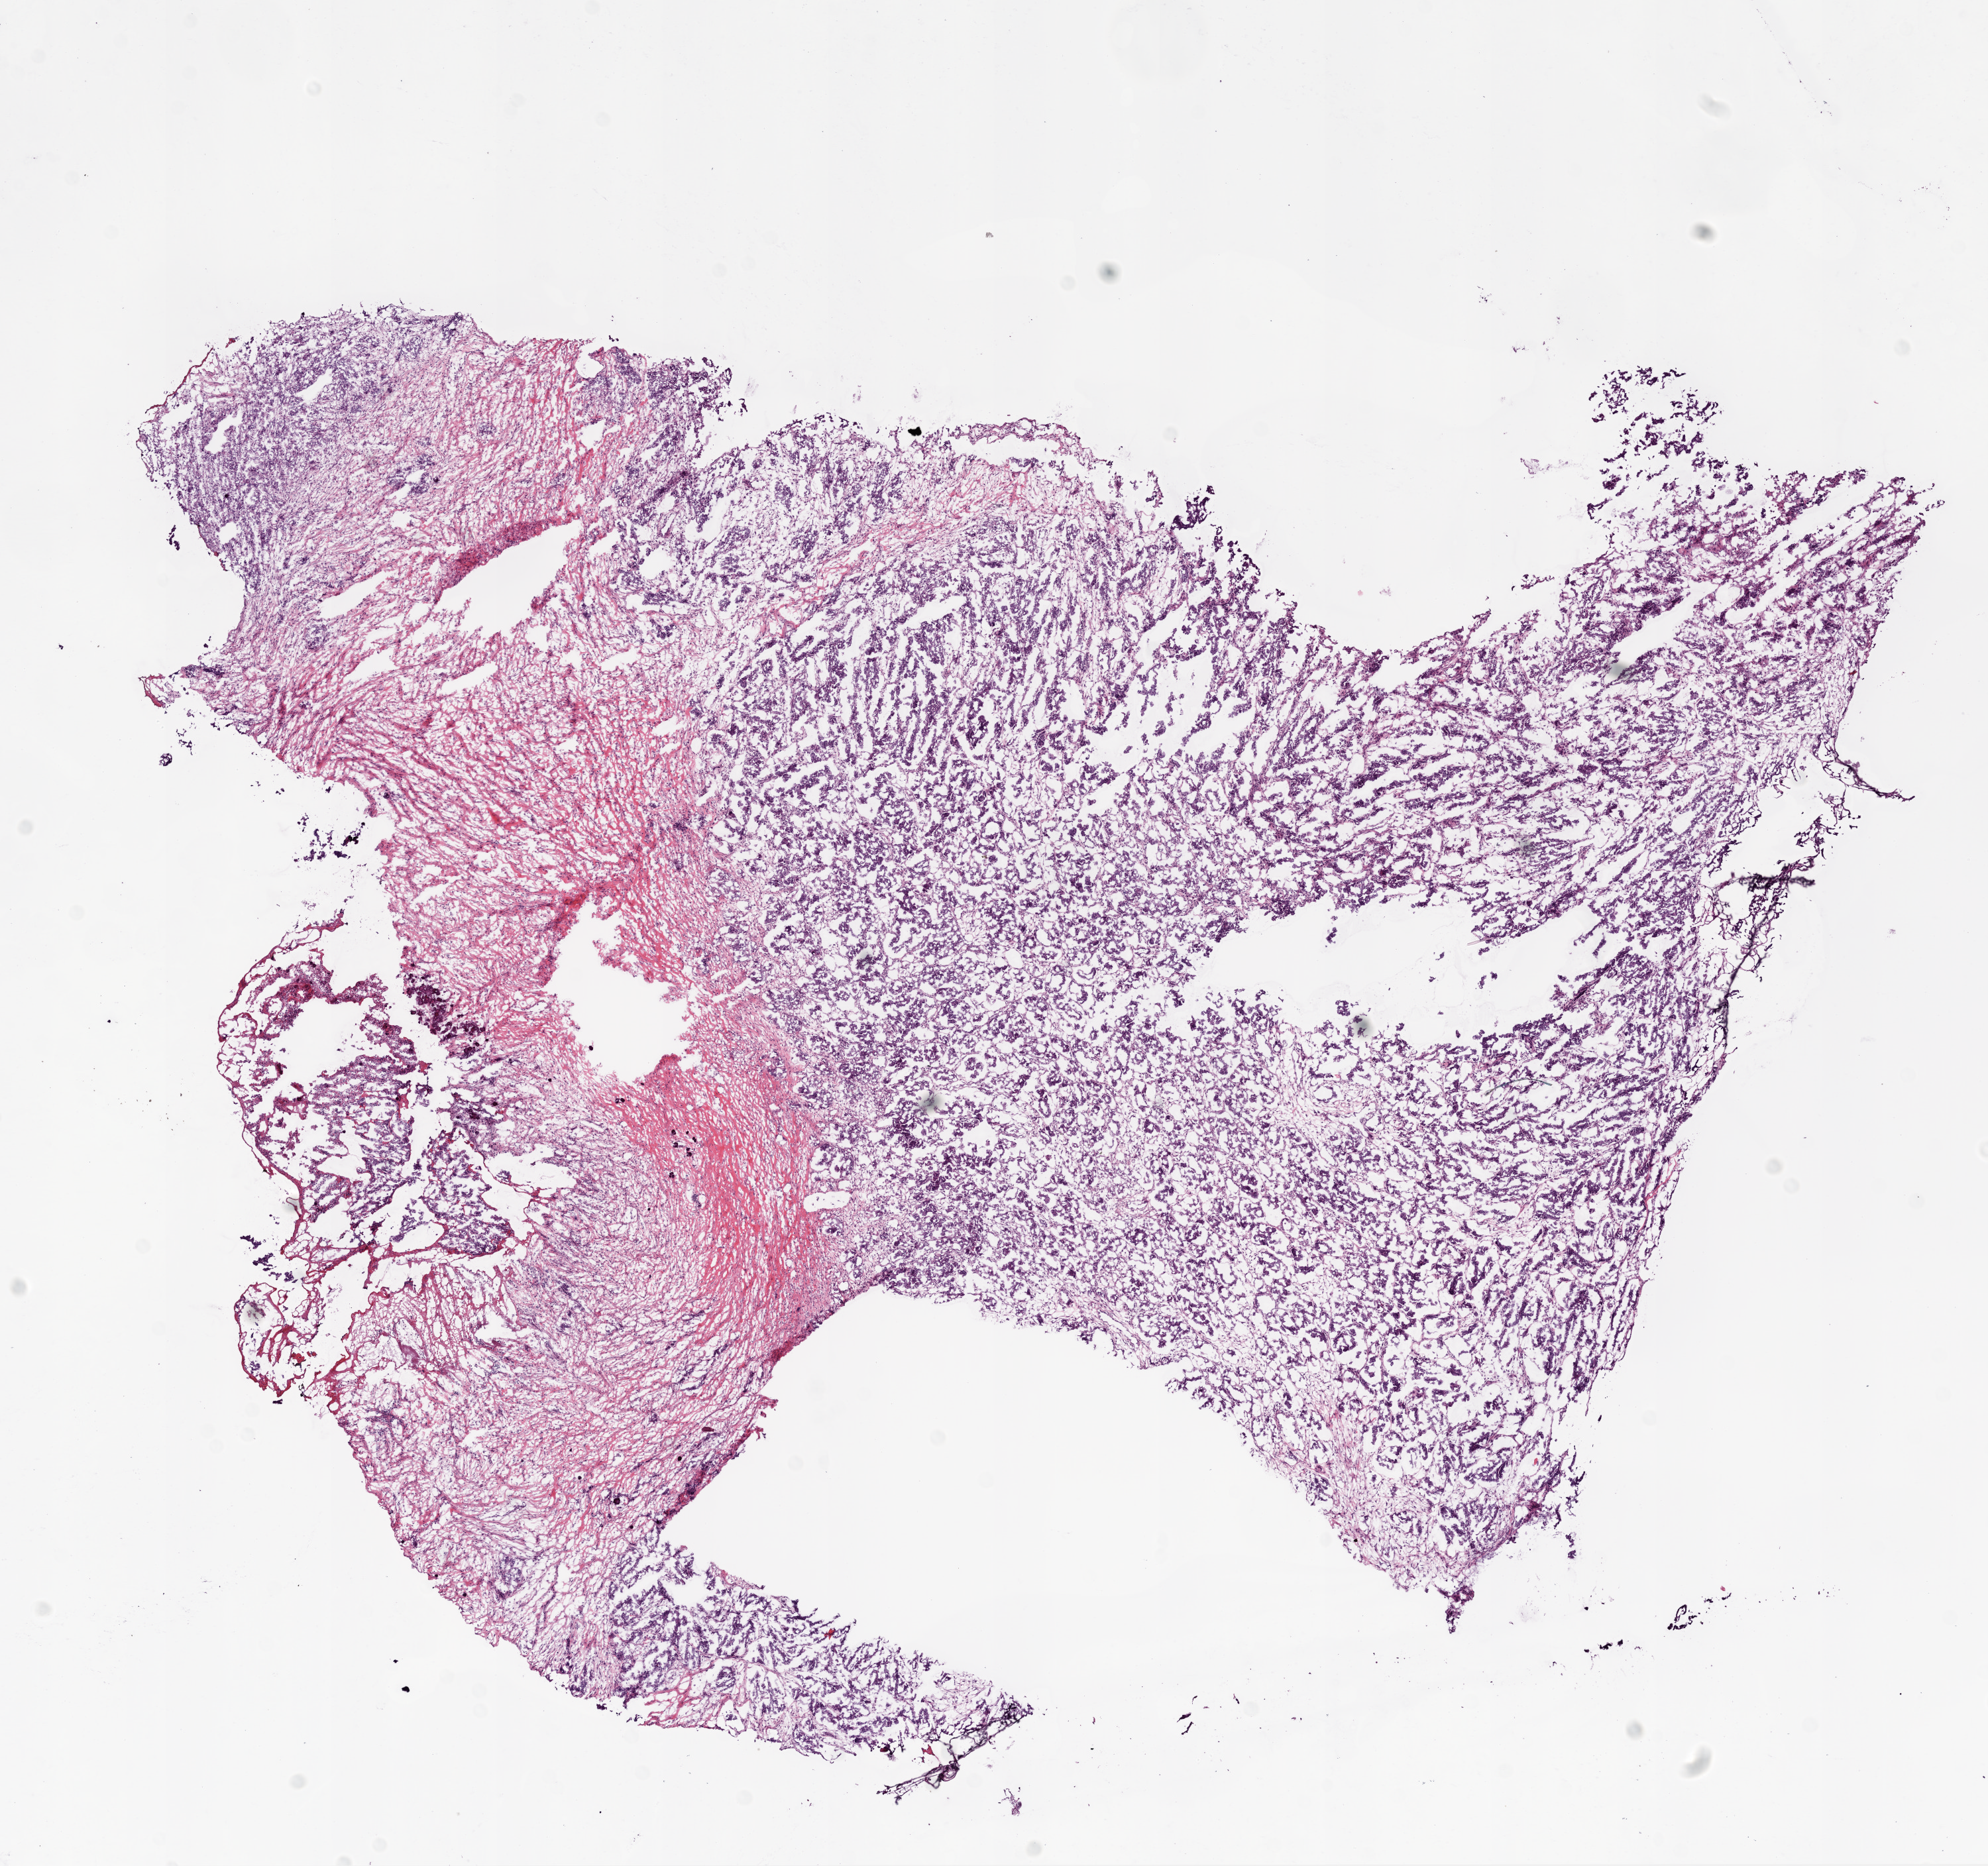
Digitized H&E tissue section (whole slide) — low-resolution overview of the scanned area, about 12.0 x 11.3 mm (slide scanned at 20x), frozen section from the bottom of the tissue portion, primary tumour sample from the ovary. Female, age 74 years at initial diagnosis. Histologic grade: G3 (poorly differentiated). Slide review estimates, as recorded: tumour cells 75%, tumour nuclei 80%, normal cells 0%, stromal cells 25%, necrosis 0%.
Laterality: bilateral. FIGO stage: IIIC. Histologic diagnosis: Serous cystadenocarcinoma, NOS.